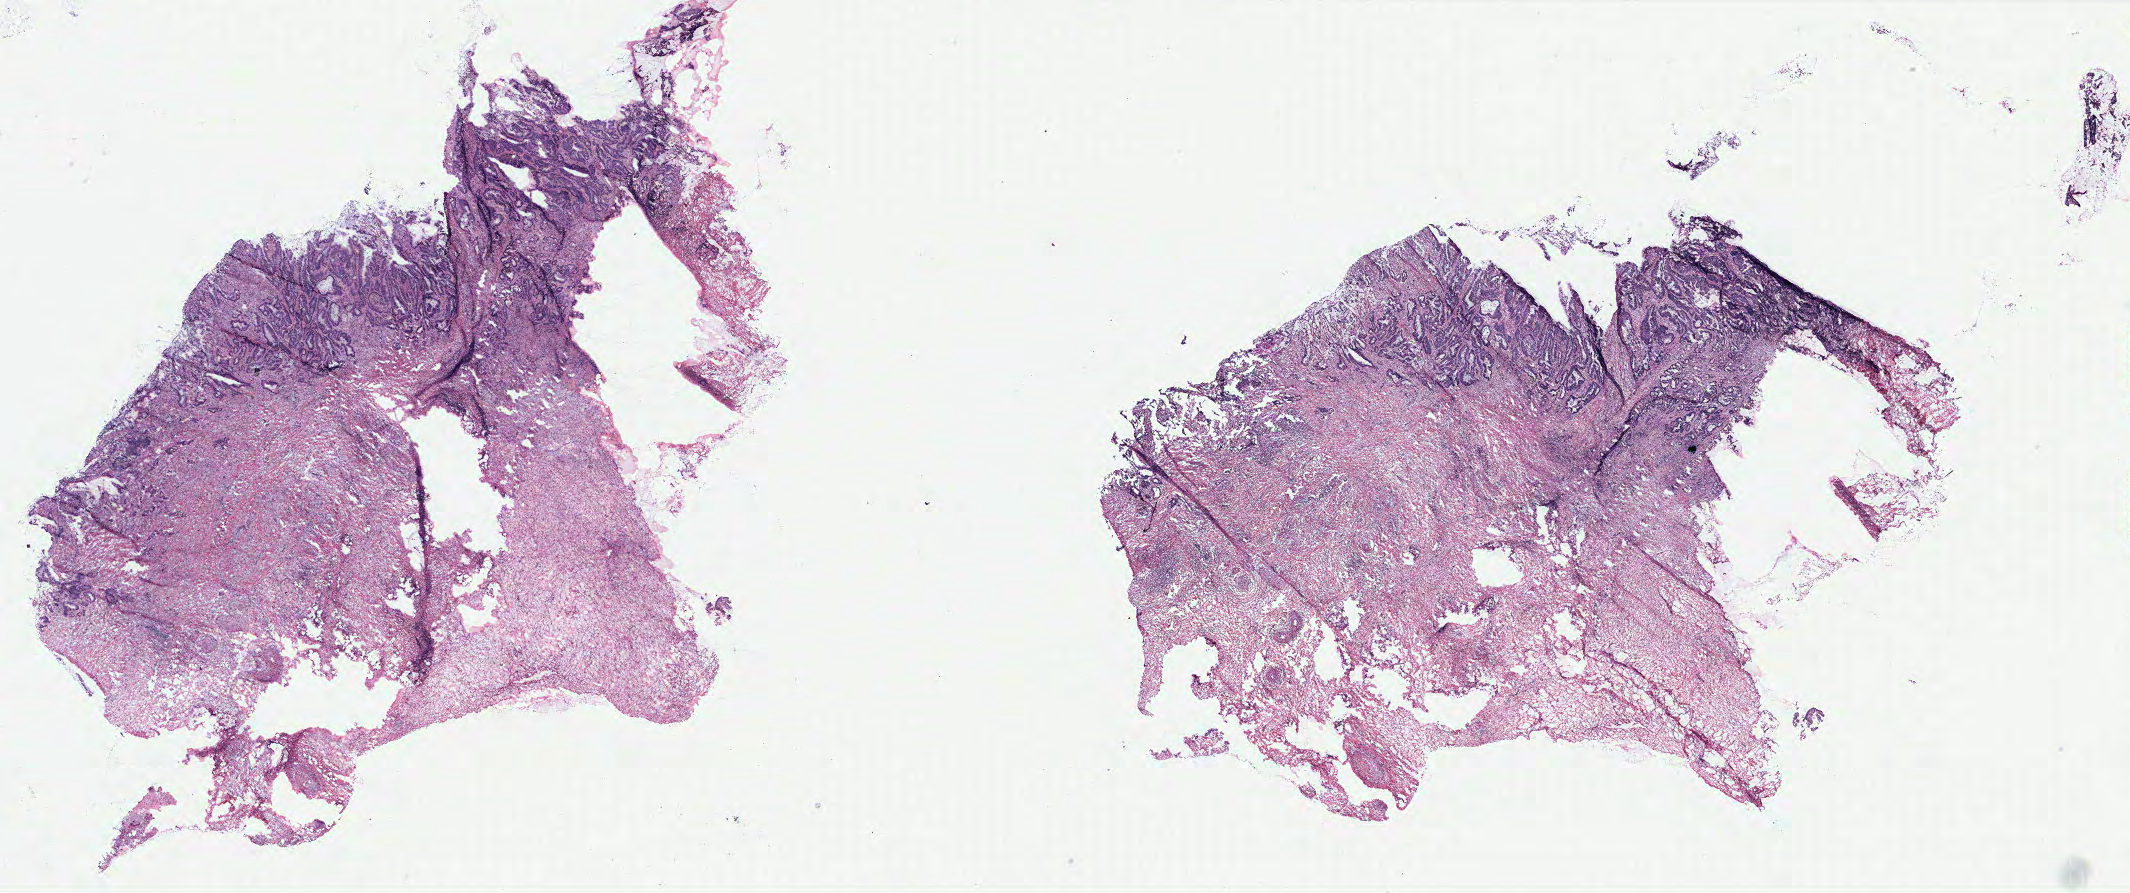
H&E whole-slide image — shown as a low-resolution overview of the whole scanned area (about 34.1 x 14.3 mm, acquisition: 40x scan). Colon, tissue type not recorded.
Patient diagnosis (cohort enrolment): colon cancer (colon).